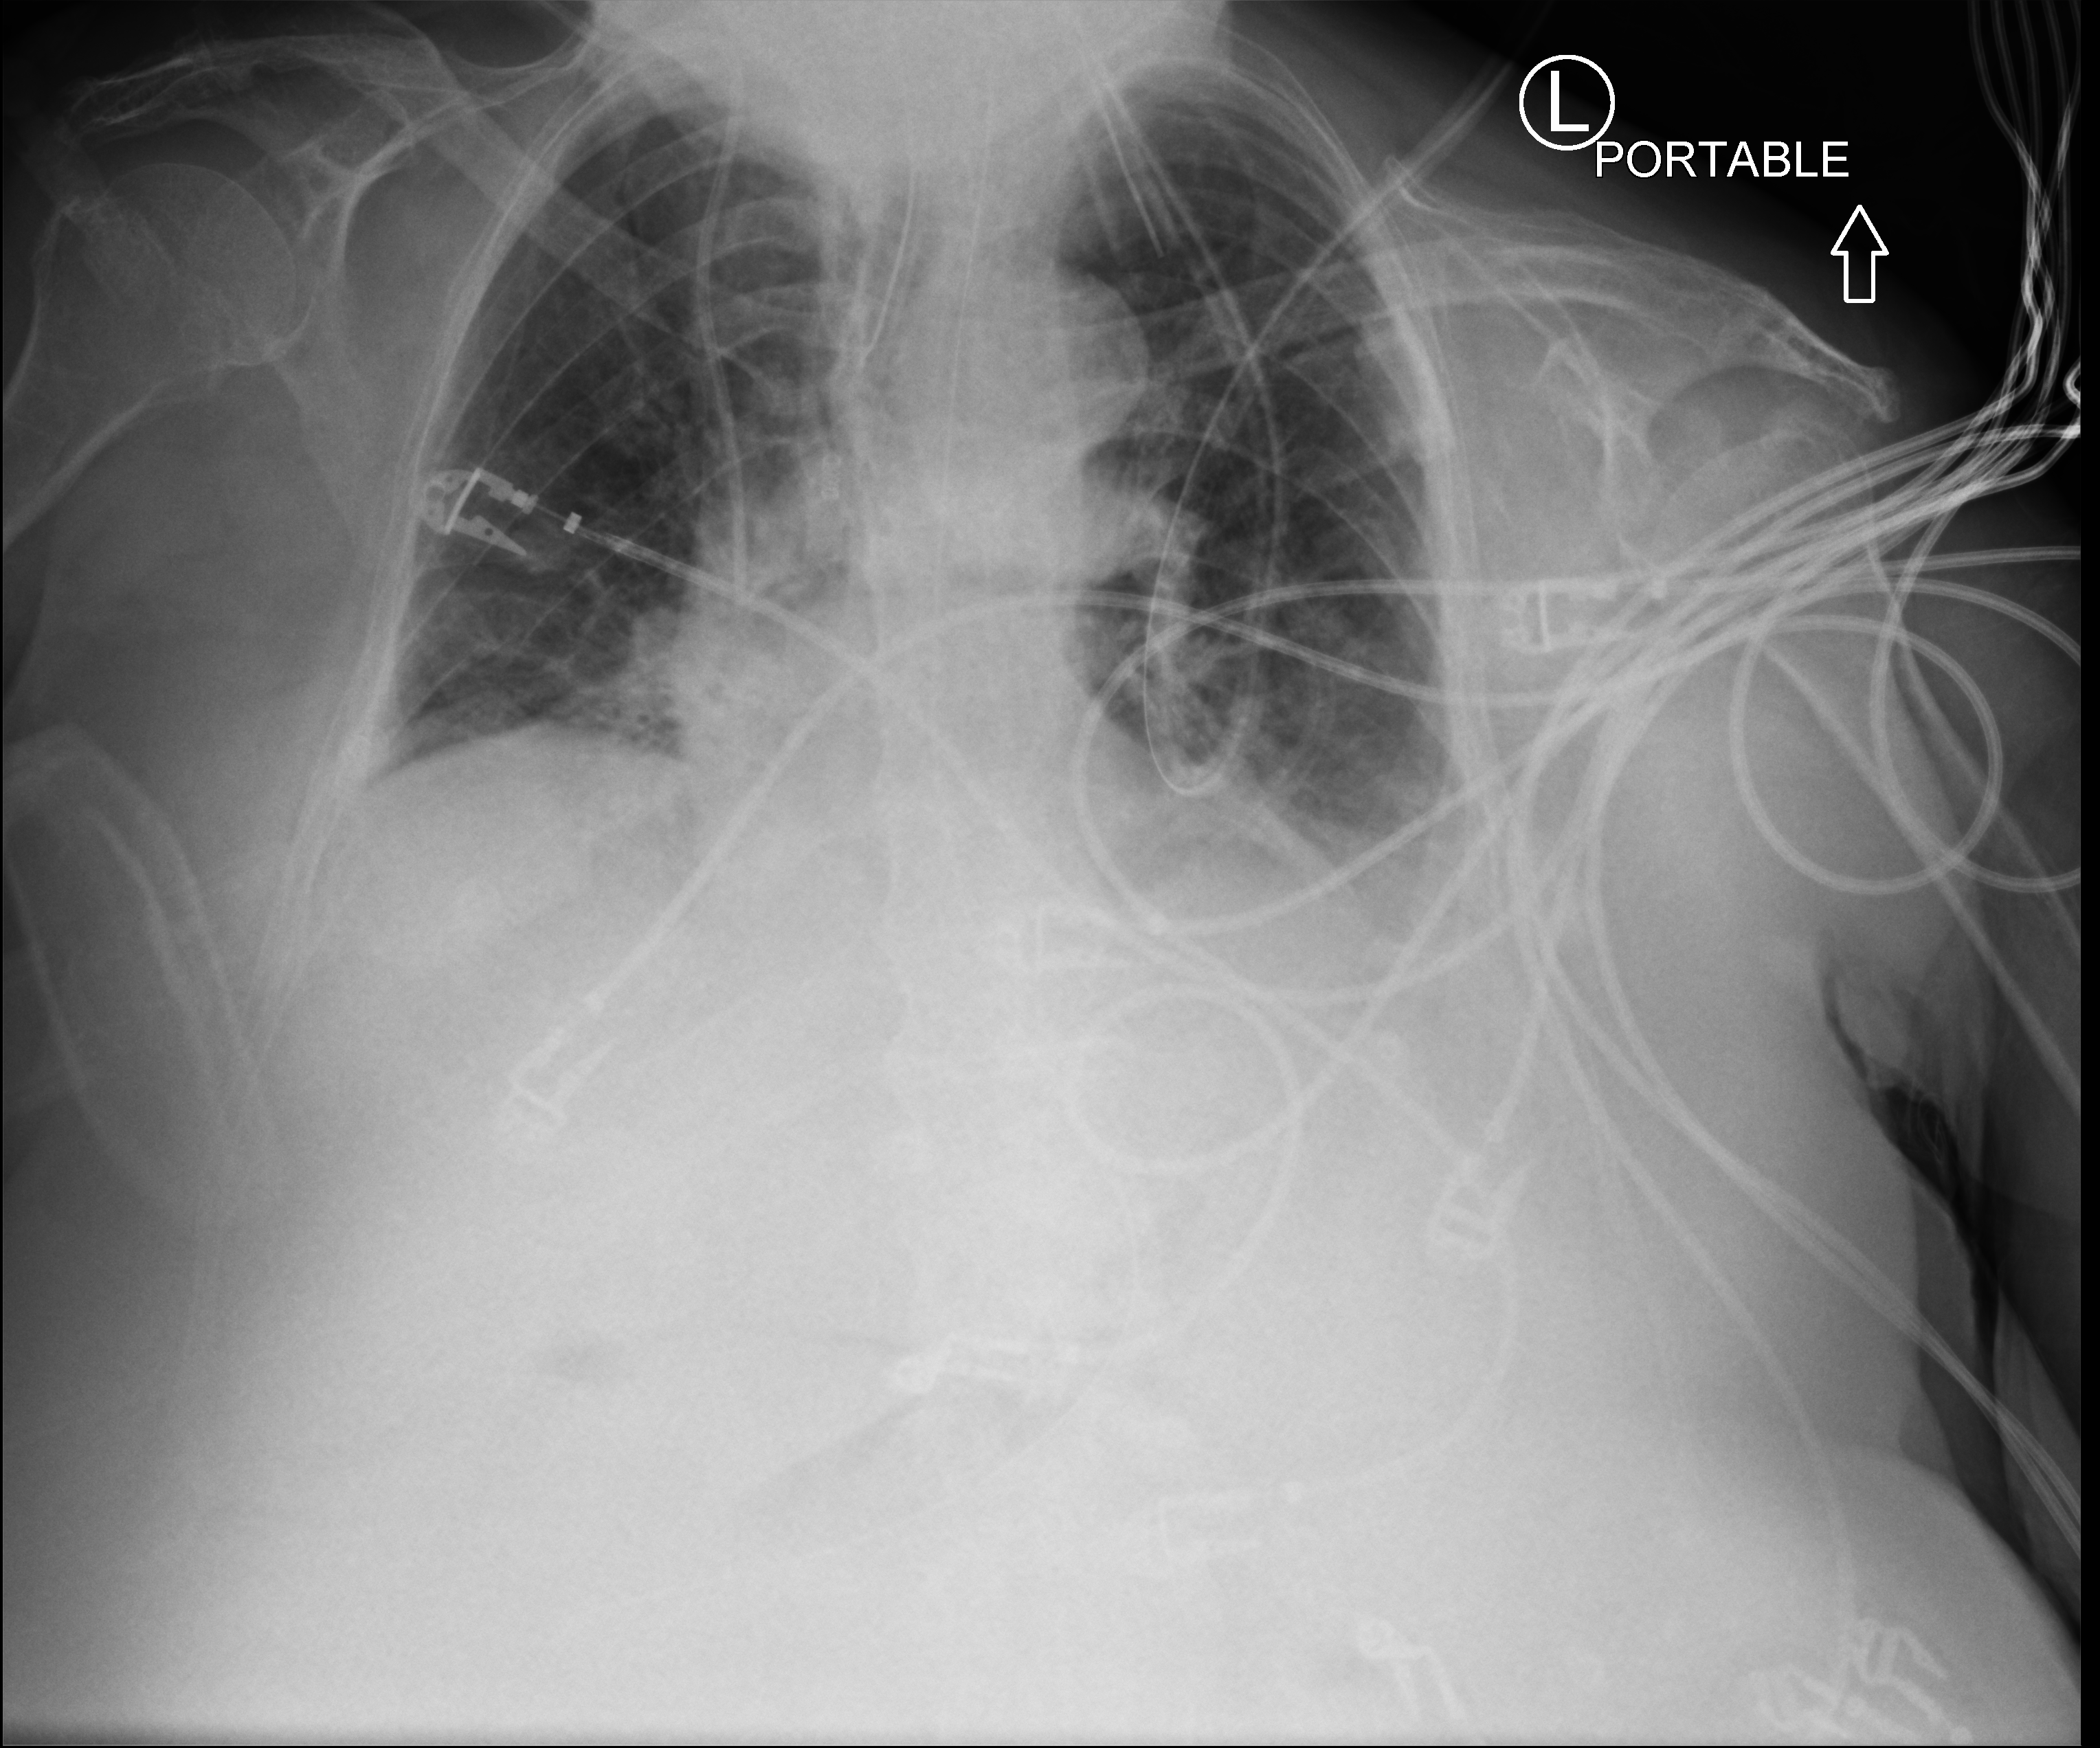
Portable chest radiograph; anteroposterior (AP) projection. Female patient hospitalised with COVID-19, age 75–90 years.
Hospital-stay facts (about this admission, not read from this image; timing relative to this image not recorded):
- other chronic lung disease (admission record): no
- mechanically ventilated during this hospital stay: yes